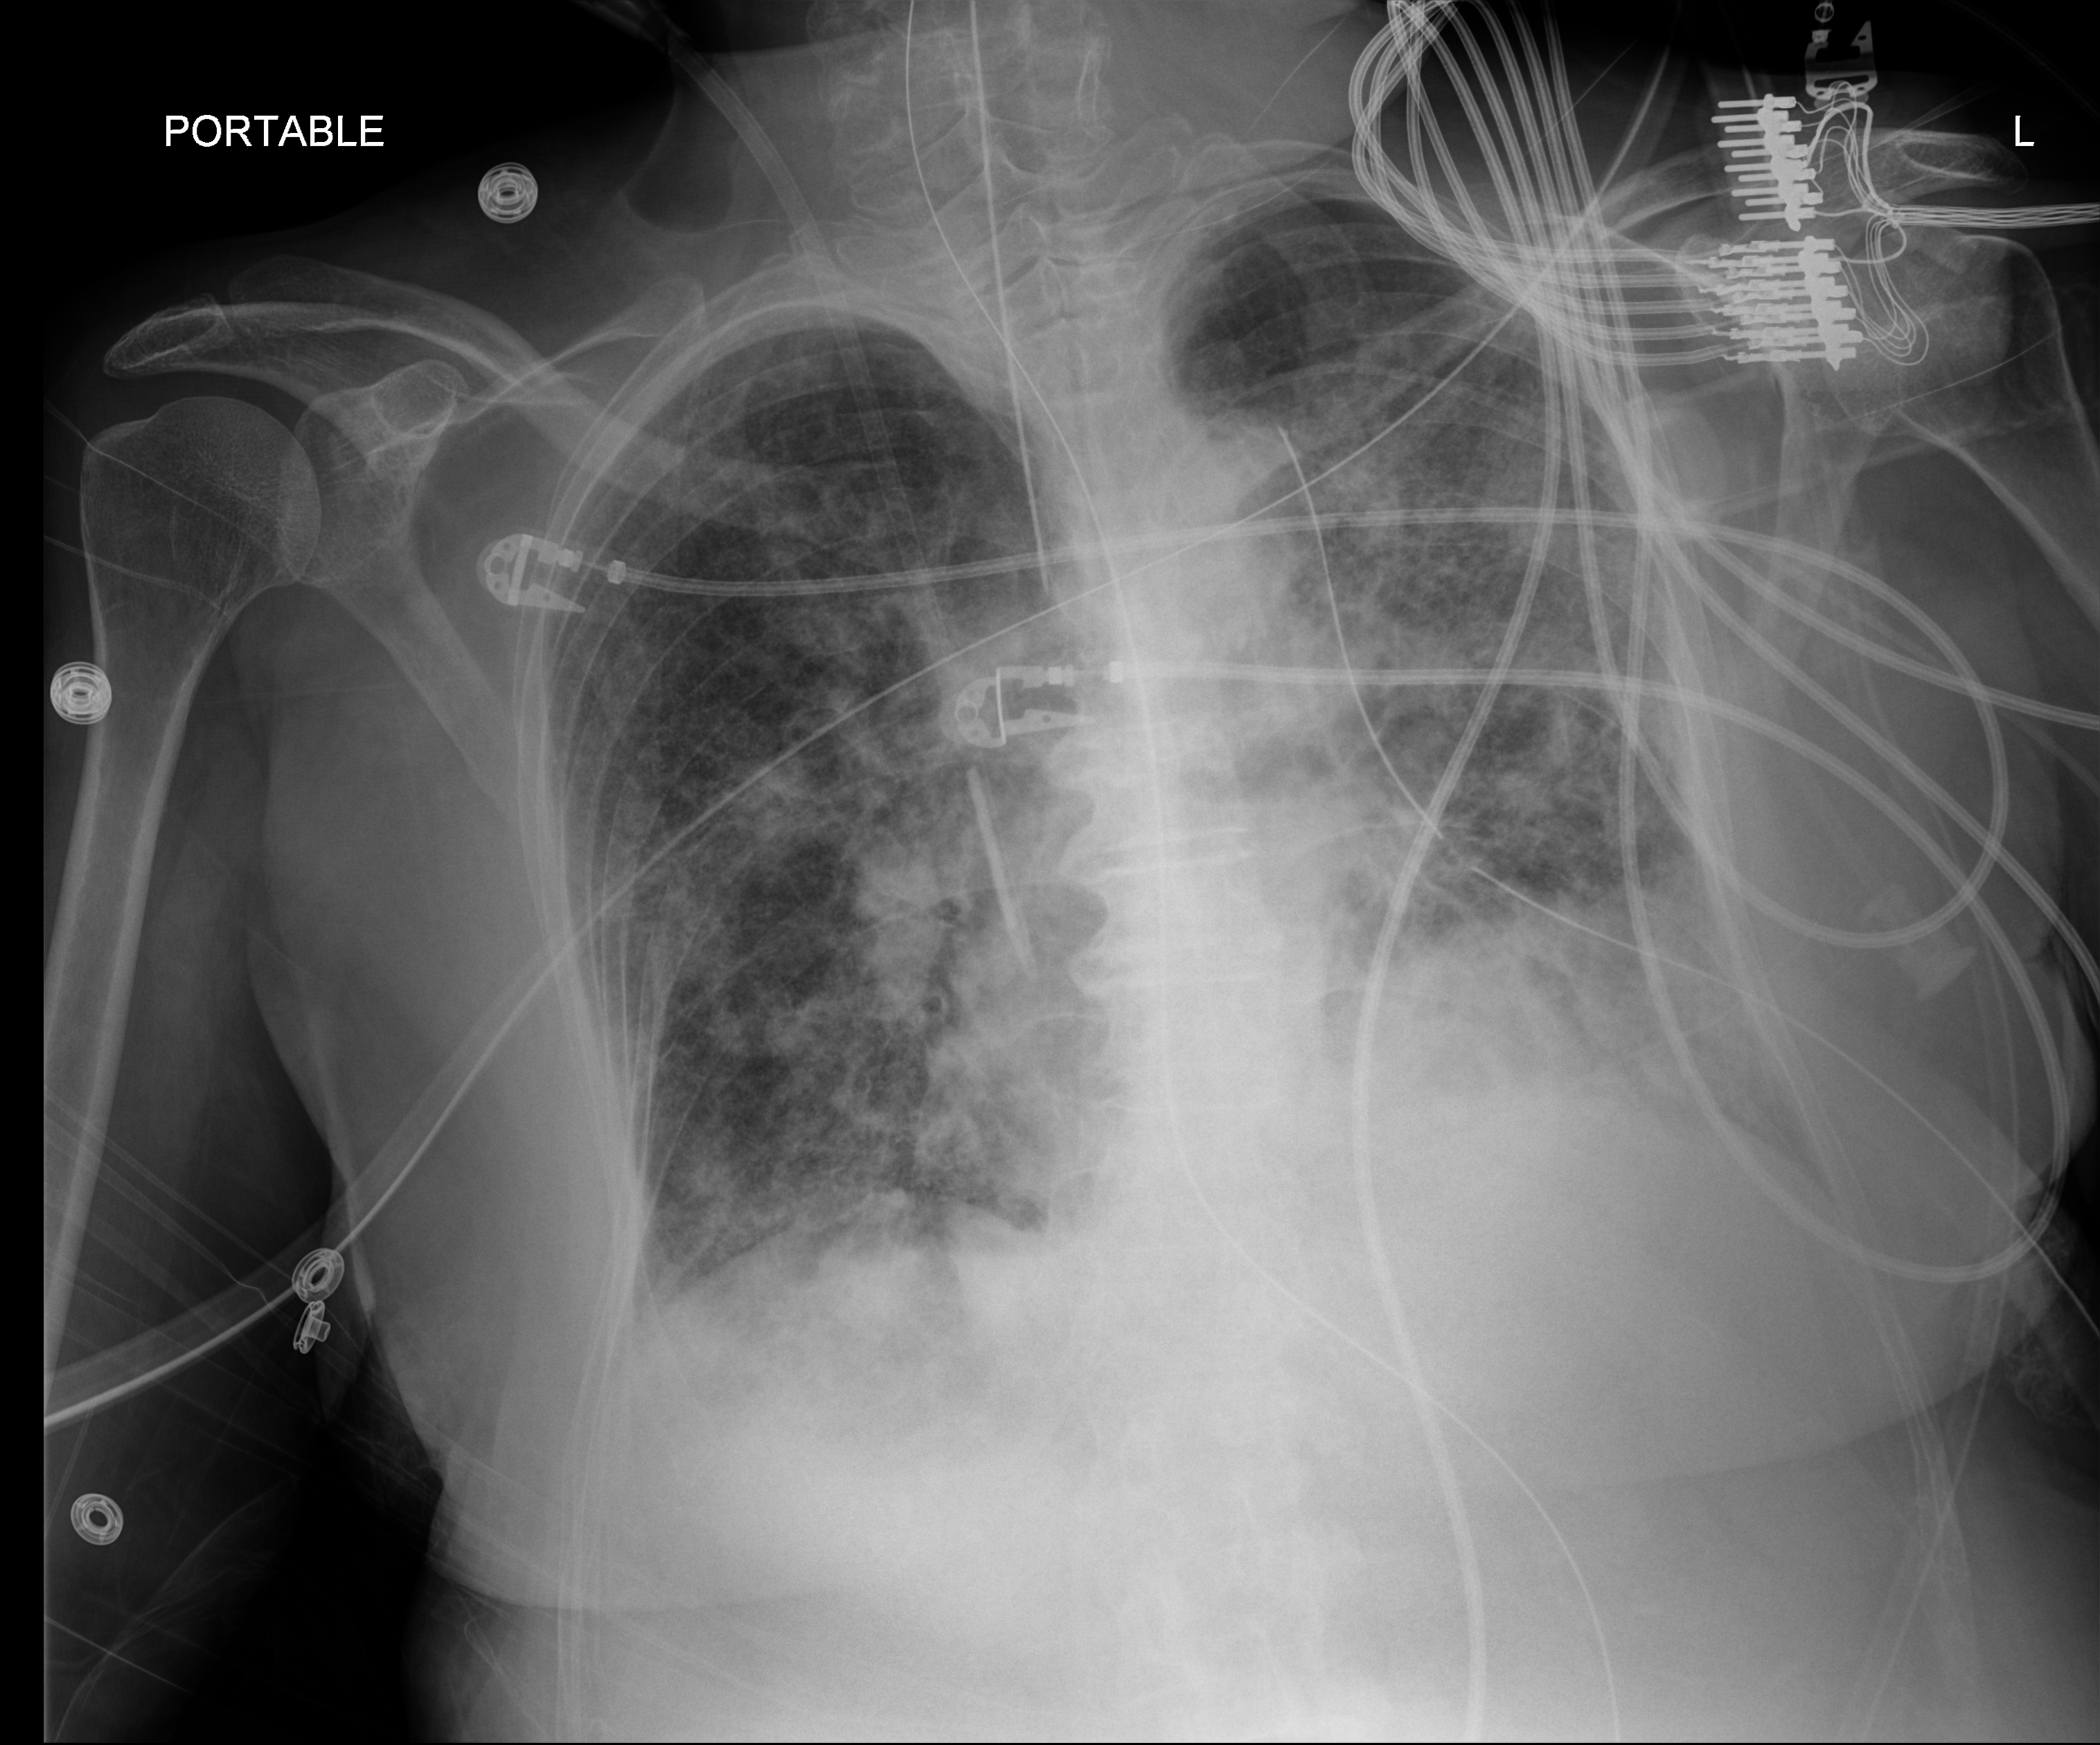
Chest X-ray (portable); anteroposterior (AP) projection. Female patient hospitalised with COVID-19, age 75–90 years.
Admission-level facts for this patient (not findings on this image; timing relative to this image not recorded): mechanically ventilated during this hospital stay: yes.